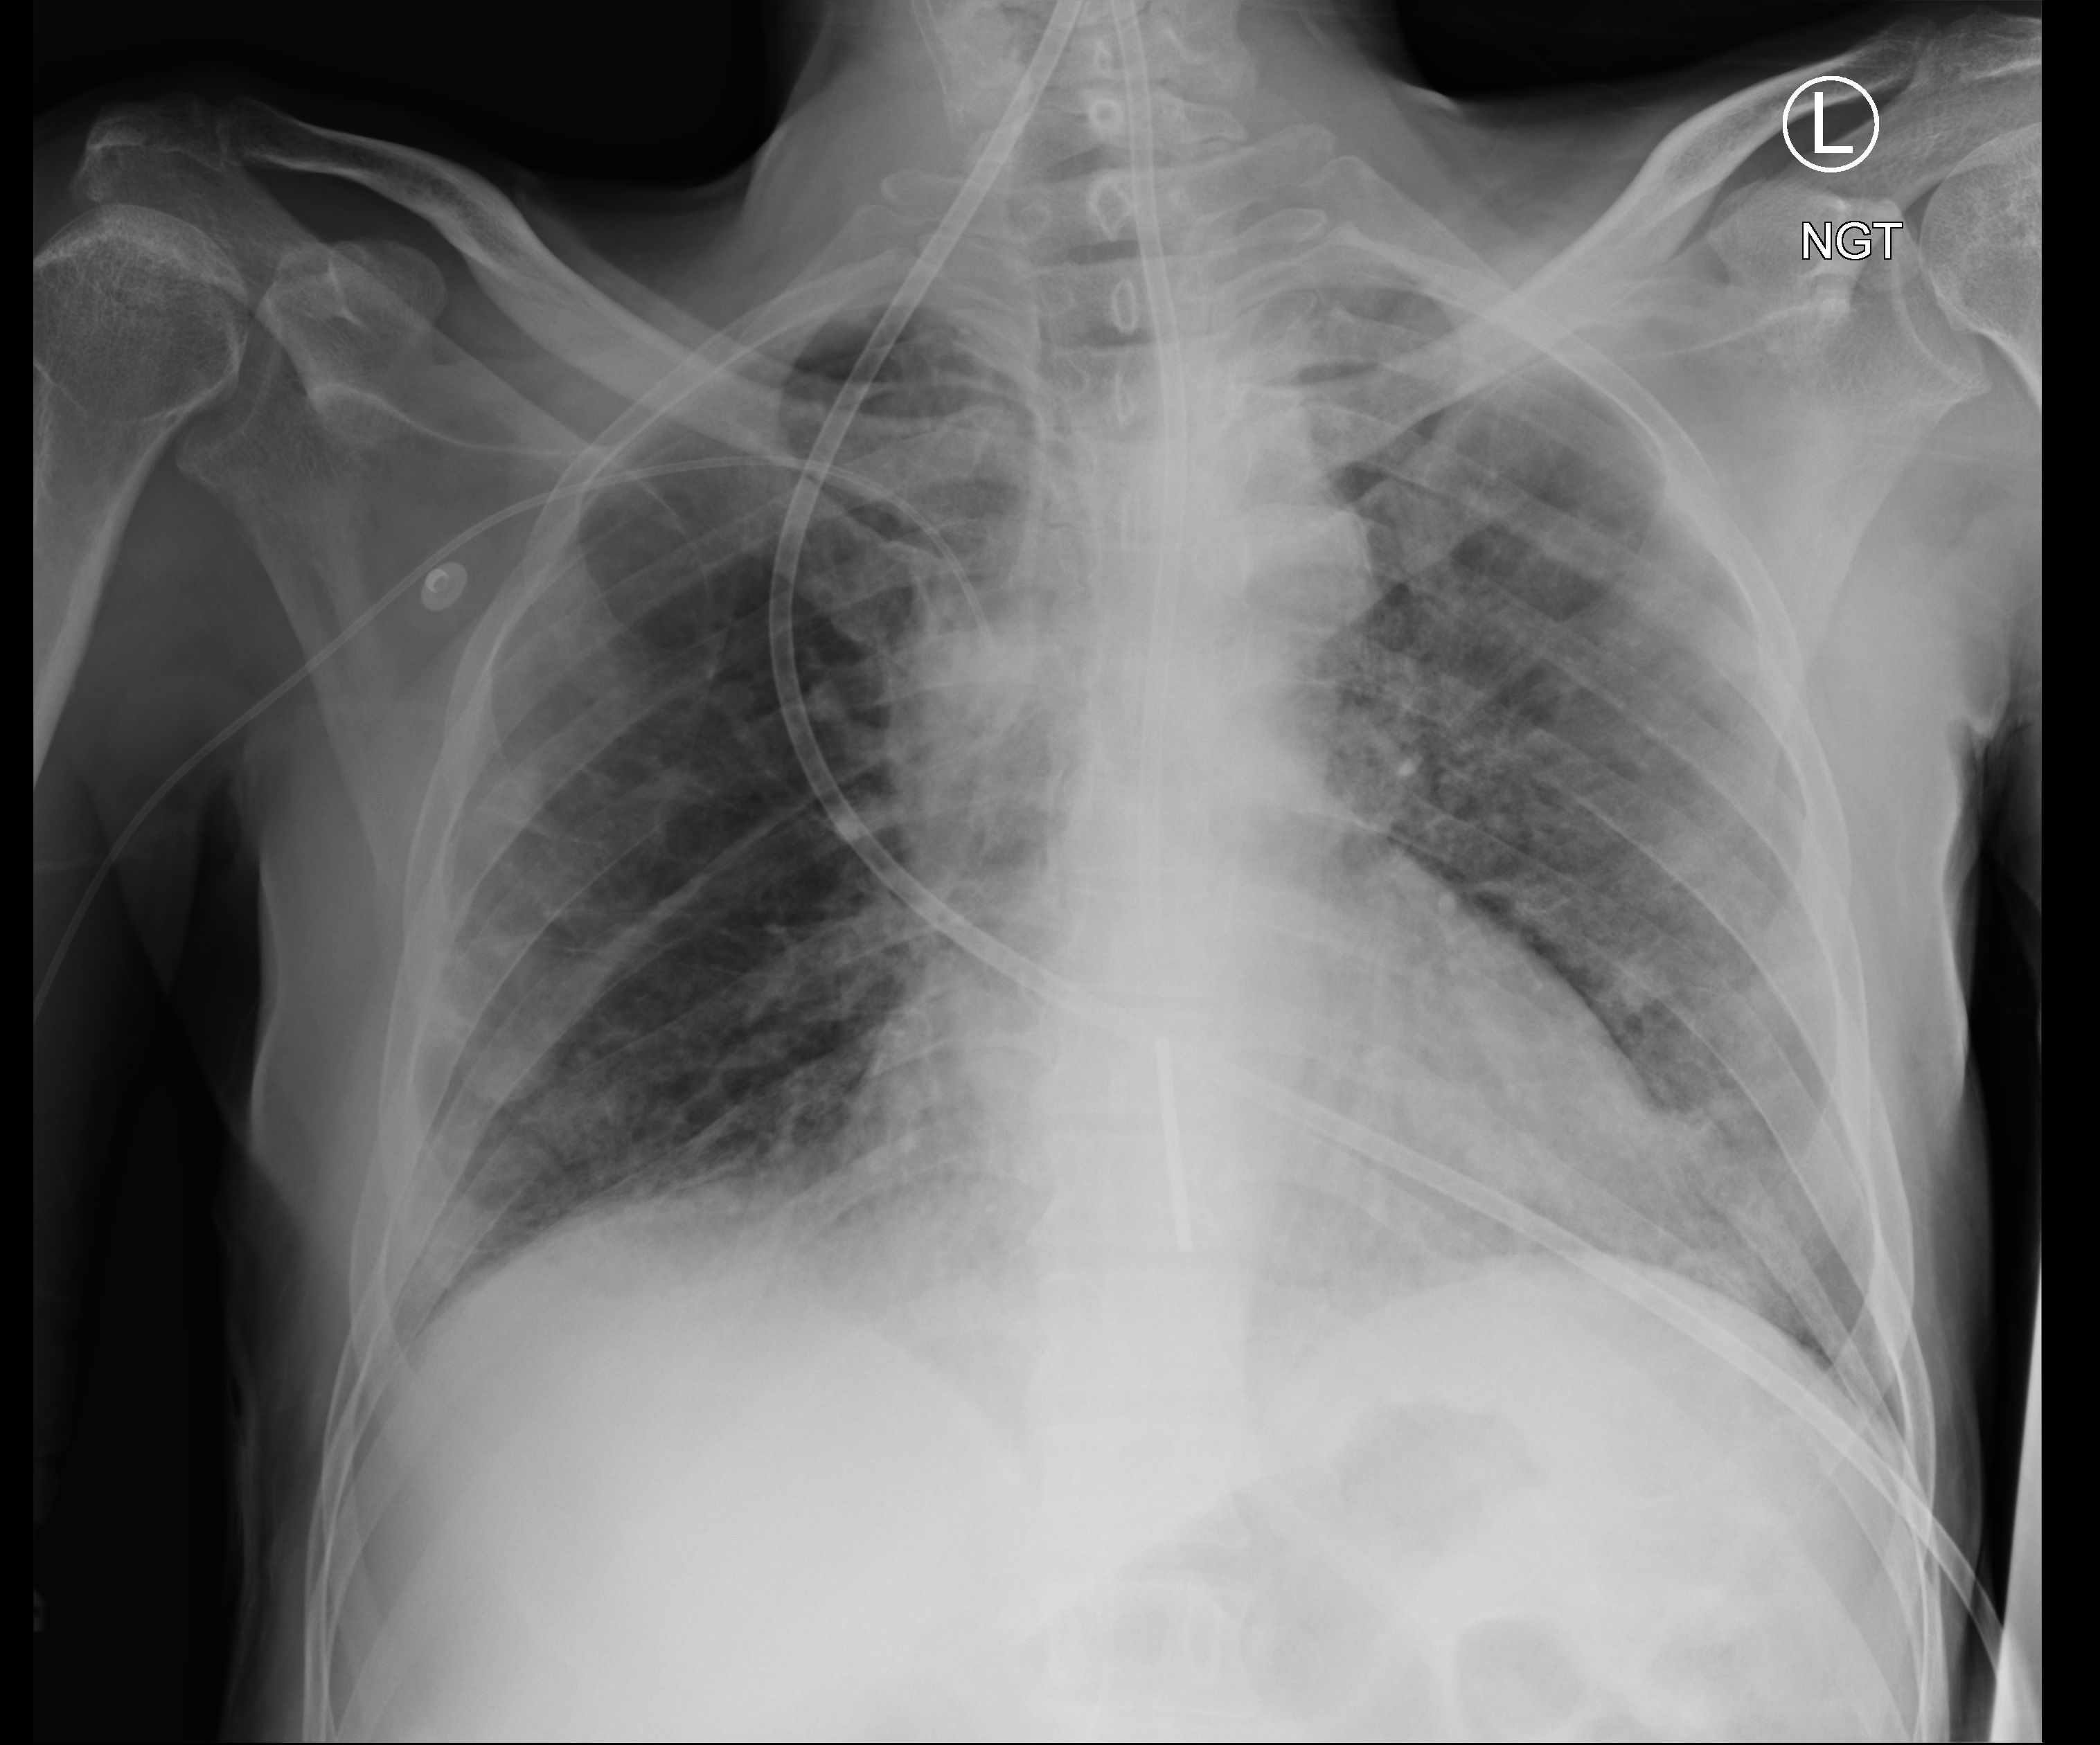
Portable chest radiograph; anteroposterior (AP) projection. Patient hospitalised with COVID-19; male, aged 18–59 years.
From the hospital-stay record, not from the radiograph (when in the stay this image was taken is not recorded): mechanically ventilated during this hospital stay: yes.